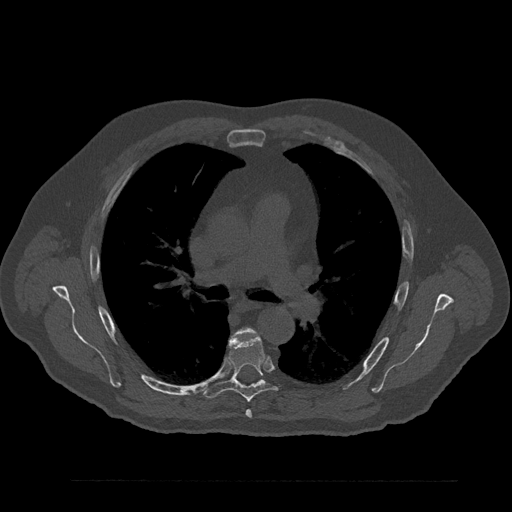
CT including the spine, one axial slice. Position 562 of 797 along the scan axis. Reconstruction kernel Br40s/3. Bone window (W 1800 / L 400 HU). 512 × 512 image matrix, field of view 430 × 430 mm. Male patient, age 61 years. Case-level facts recorded for this patient, not image findings: primary cancer: prostate.
Structures marked on this image (semi-automatic segmentation, software-assisted and operator-edited):
- T5 vertebra: bounding box (x1, y1, x2, y2) in pixels: (238, 329, 252, 418)
- T6 vertebra: (204, 334, 278, 402)